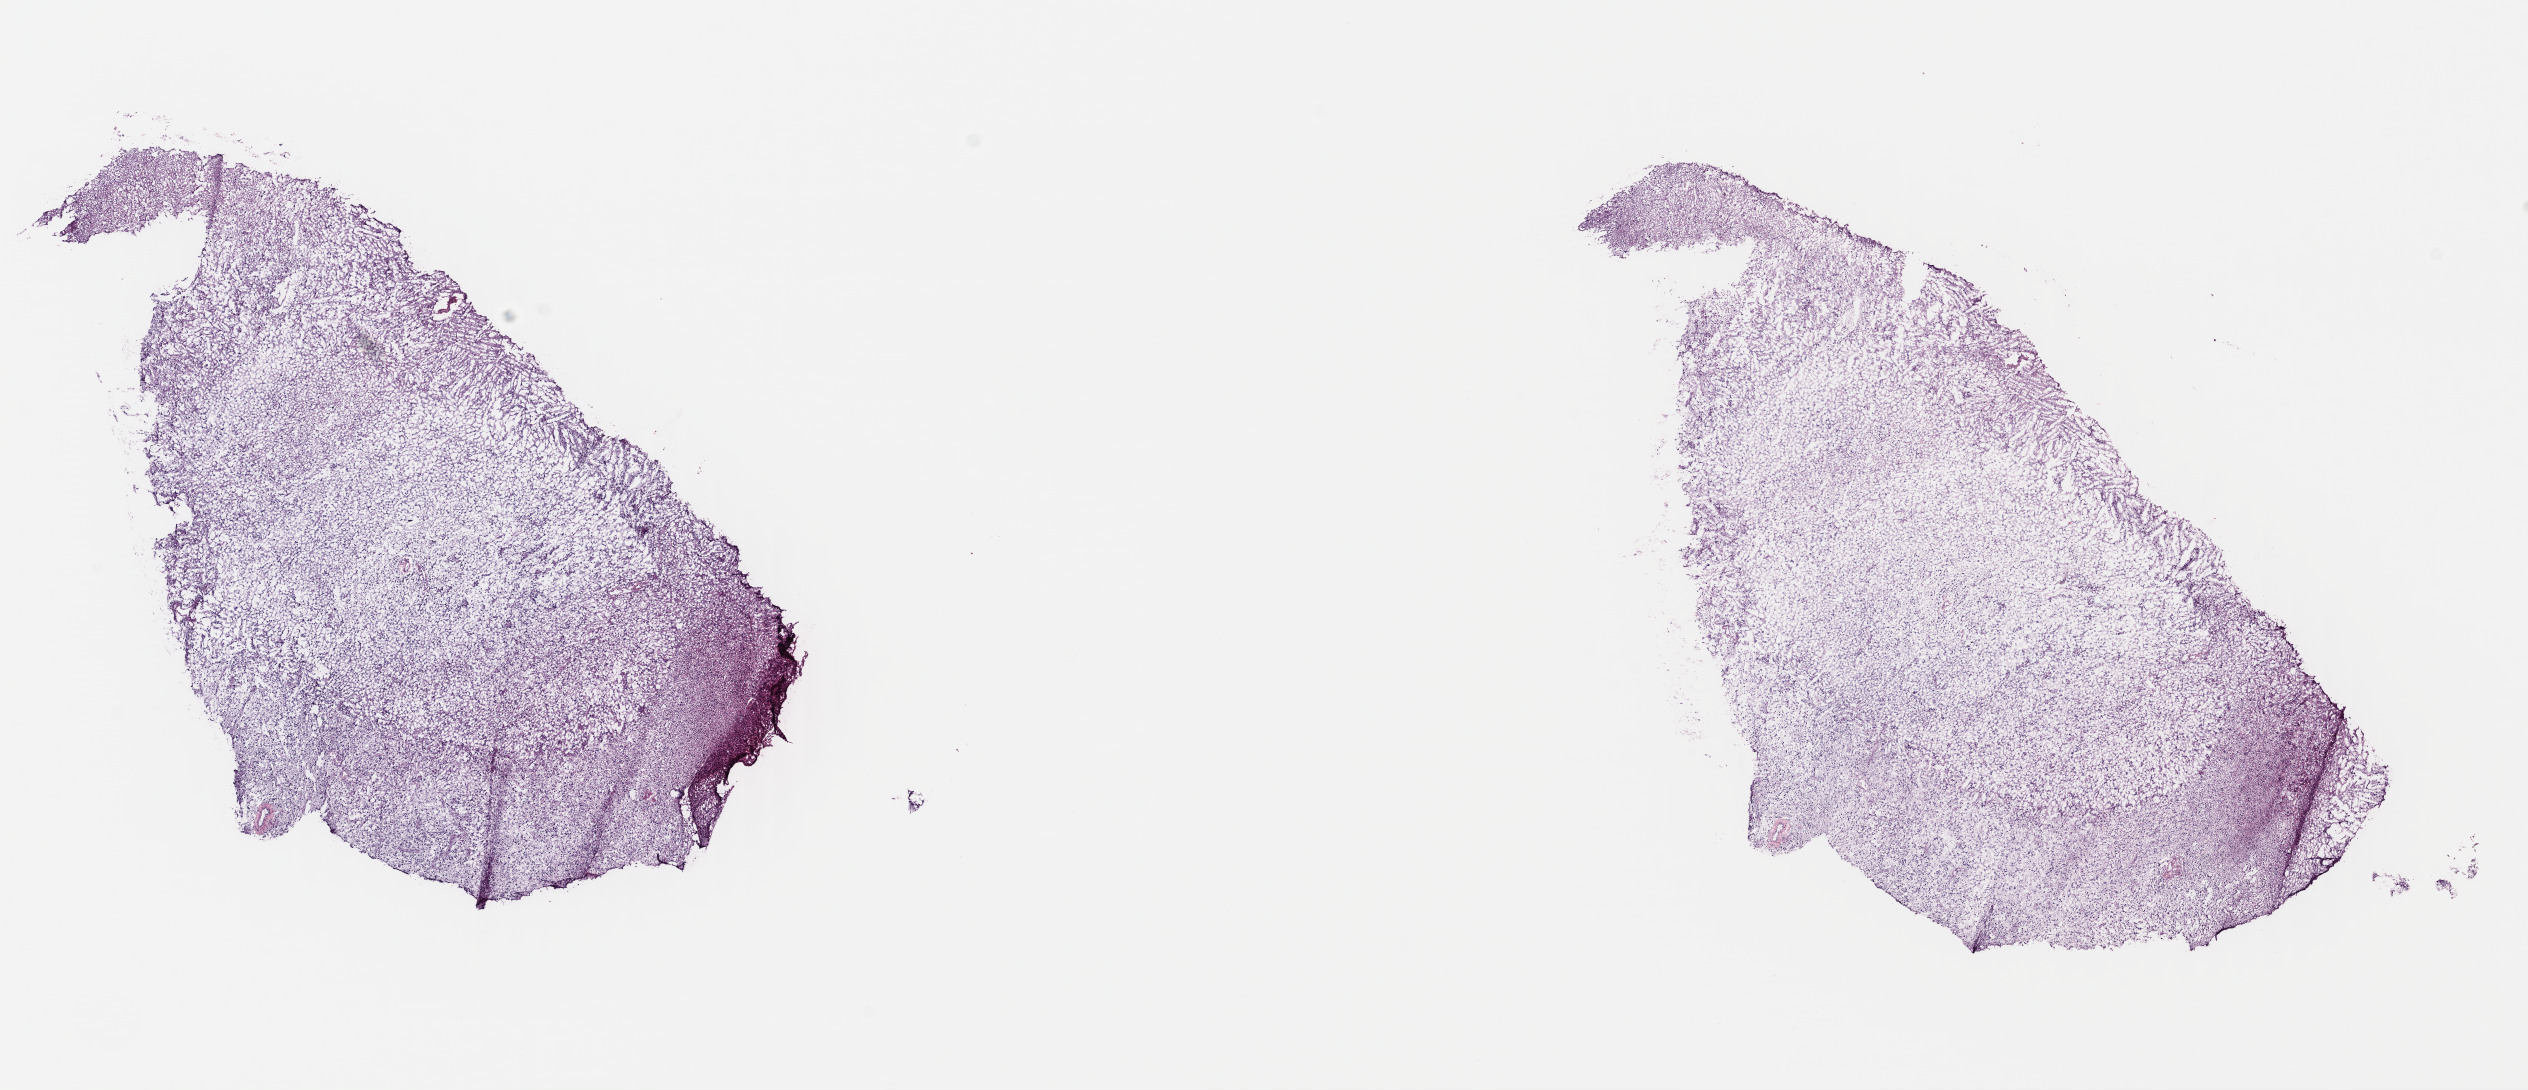
Whole-slide histology image, Hematoxylin and eosin (H&E) stained, shown as a low-resolution overview of the whole scanned area (about 19.9 x 8.6 mm); frozen section from the top of the tissue portion; brain, primary tumour sample. Male, age 38 years at initial diagnosis. Histologic grade: G2 (moderately differentiated). Composition of this section per pathologist review: tumour cells 40%, tumour nuclei 80%, normal cells 10%, stromal cells 50%, necrosis 0%. Infiltration values recorded for this section: lymphocyte infiltration 0%, monocyte infiltration 0%, neutrophil infiltration 0%.
- pathologic diagnosis: Astrocytoma, NOS (cerebrum)